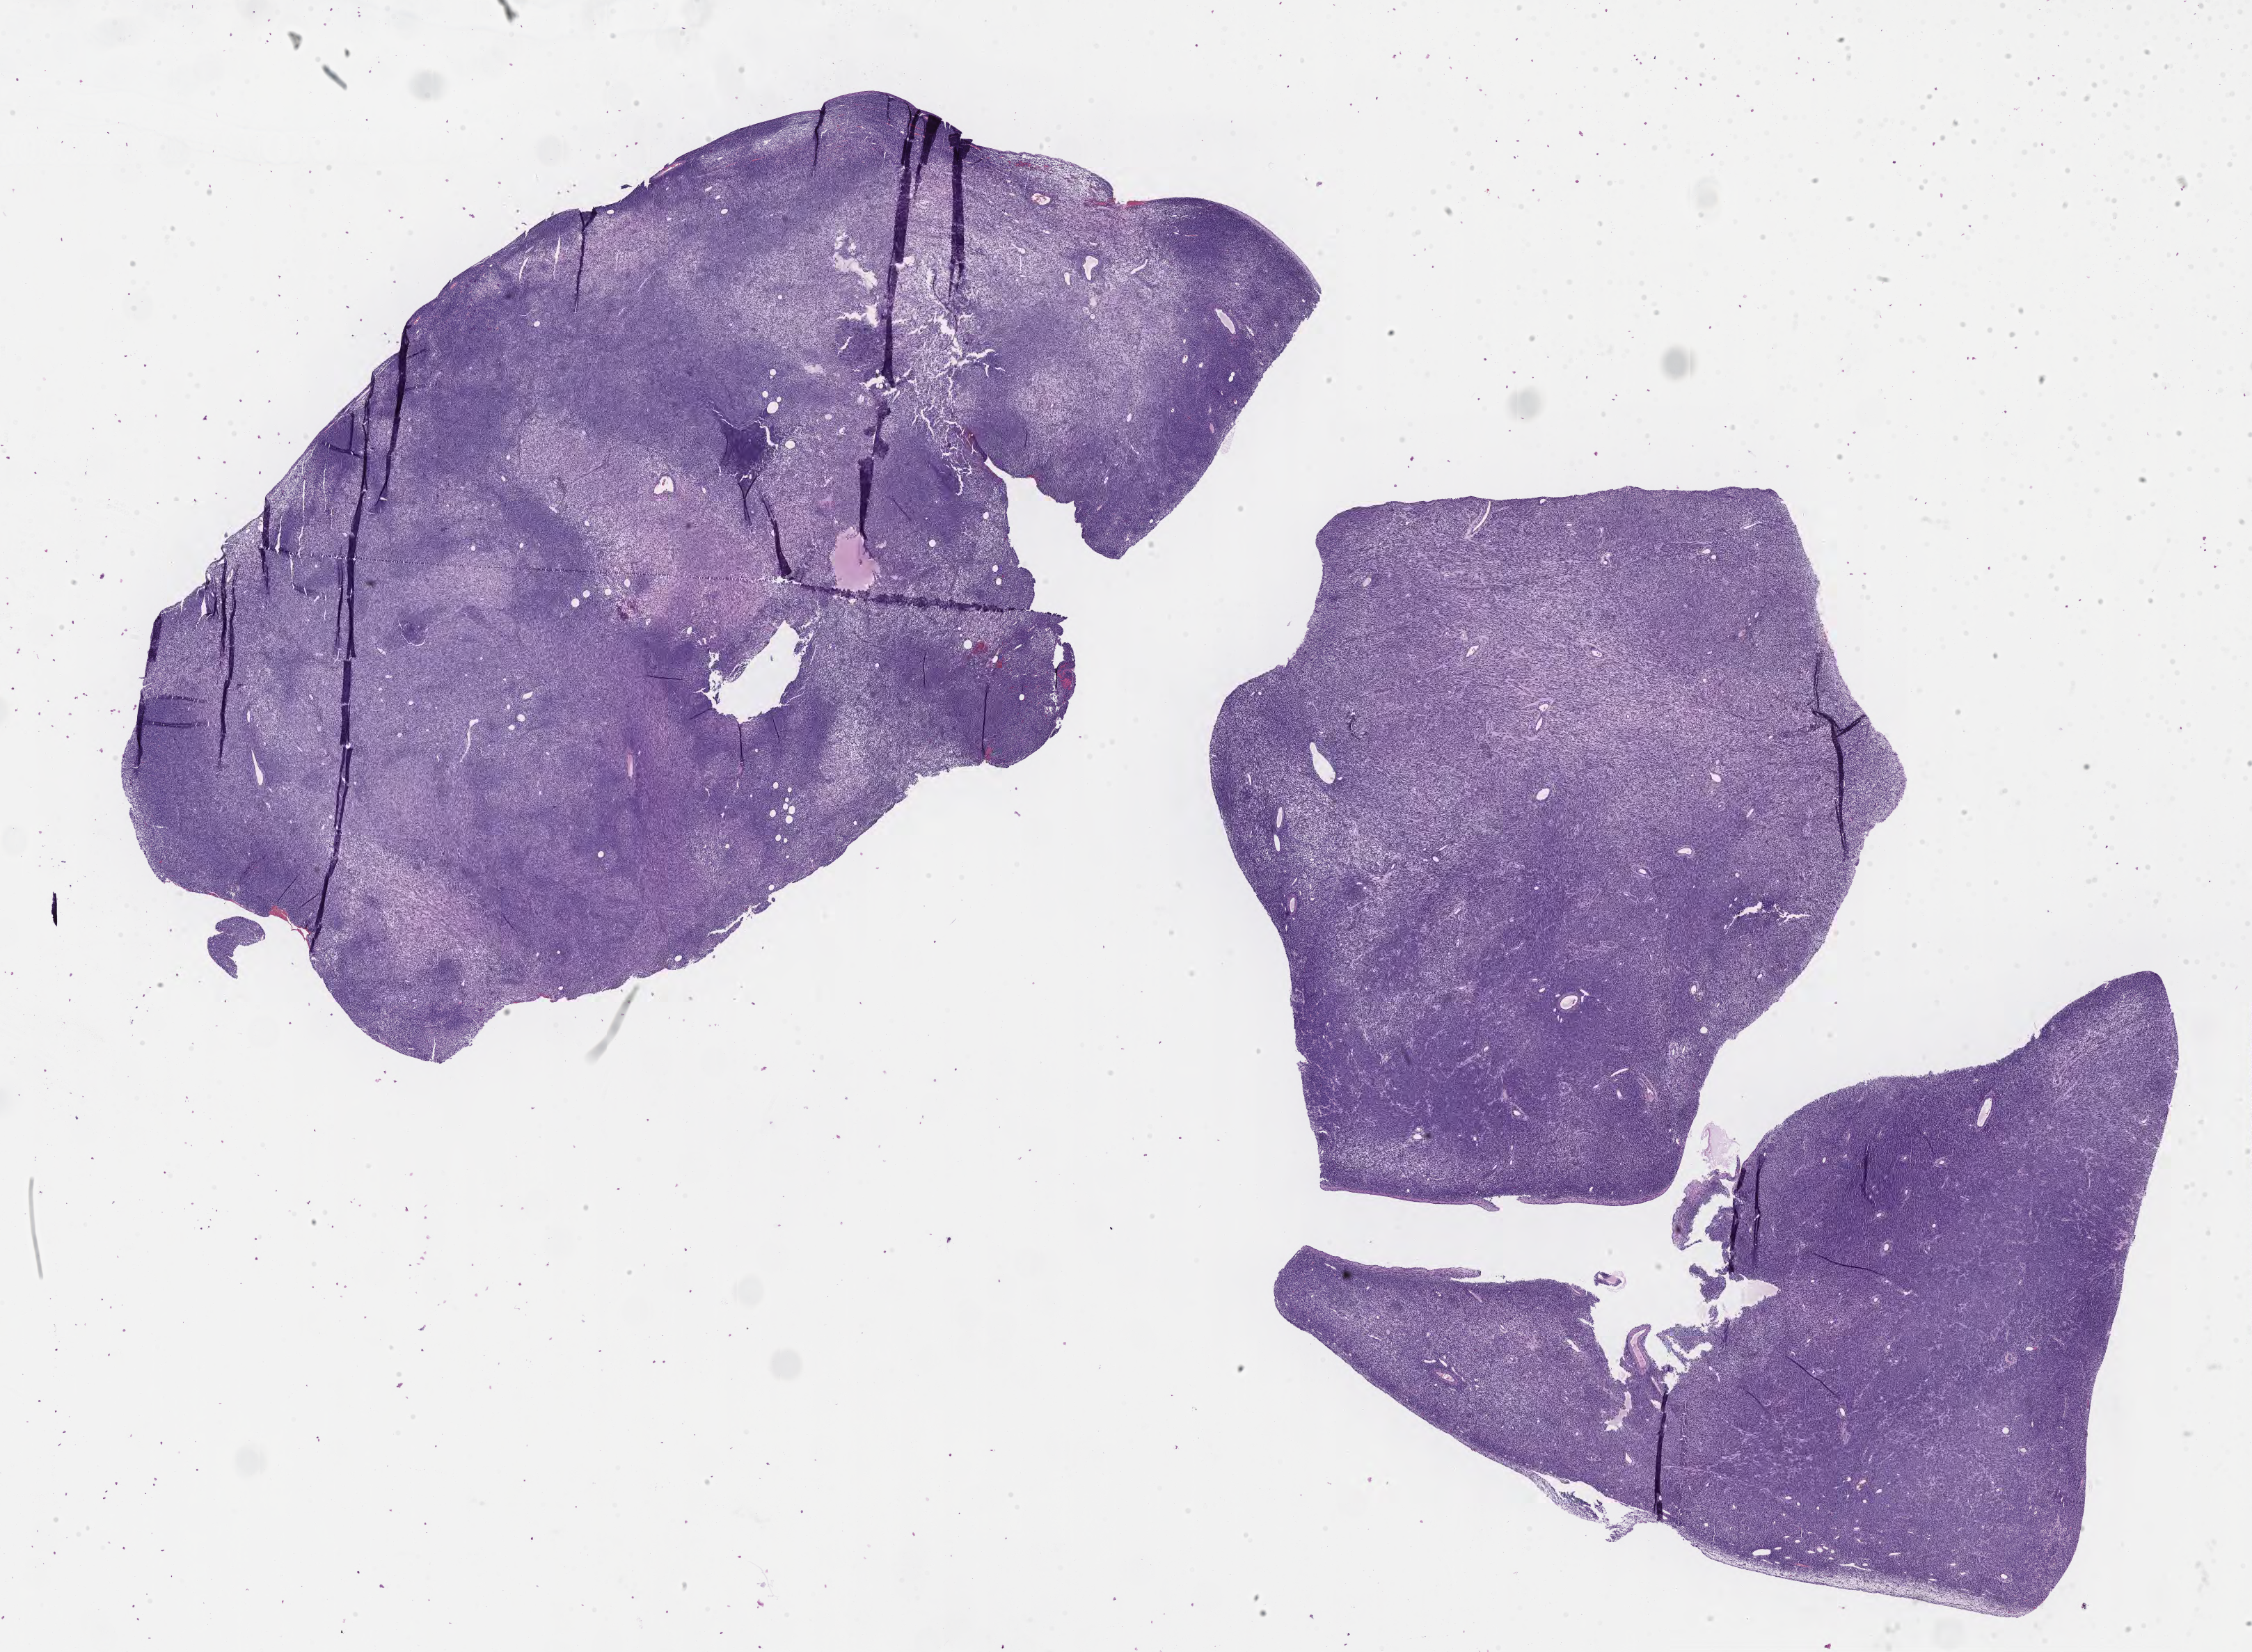
Whole-slide image, haematoxylin and eosin stain of tumor tissue from the uterus, whole scanned area (about 26.2 x 19.2 mm) shown as a low-resolution overview, formalin-fixed paraffin-embedded section. Female patient, age 251 months (20 years 11 months).
Recorded diagnosis: Embryonal rhabdomyosarcoma, NOS.